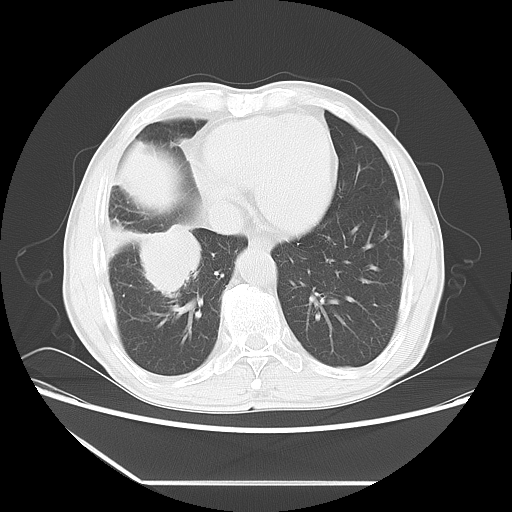
Chest CT, one axial slice; slice 20 of 60 in the series (ordered by position); lung window (W 1500 / L -600 HU); 5 mm slice thickness; 512 × 512 image matrix, field of view 386 × 386 mm. Patient: male, 72 years. Case-level facts recorded for this patient, not image findings: clinical TNM (as recorded): T1c N0 M0.
Annotated regions visible in this slice (bounding box drawn by a radiologist):
- lung tumour (recorded histology: squamous cell carcinoma): bounding box (x1, y1, x2, y2) in pixels: (122, 223, 205, 309)